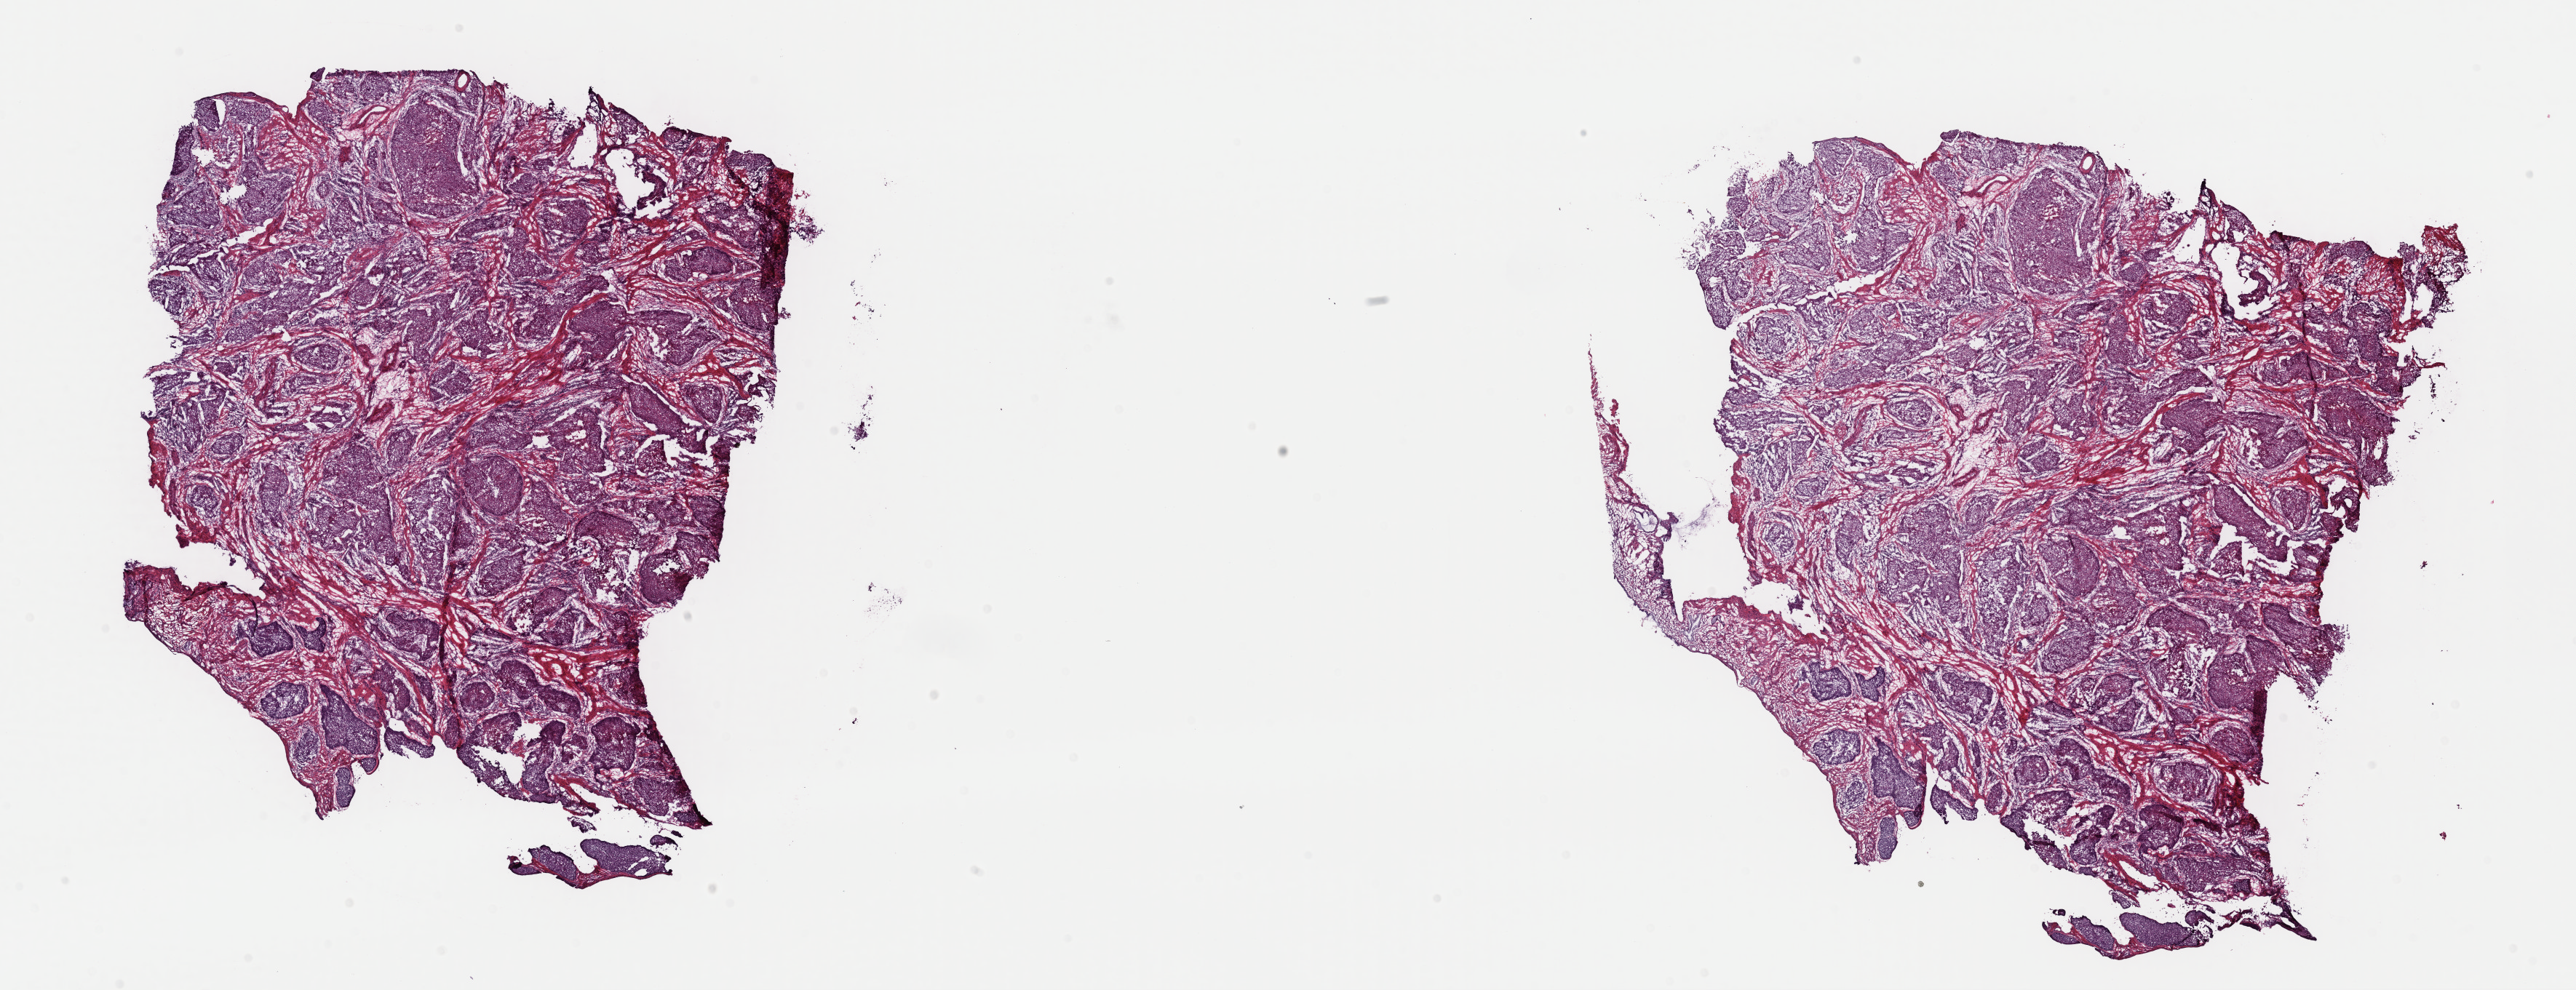
Whole-slide histology image, H&E, whole scanned area (about 28.0 x 10.7 mm) shown as a low-resolution overview, frozen section, sample: primary tumour, cervix. Patient: female, age at initial diagnosis 27 years. Histologic grade: G2 (moderately differentiated). Pathologist review of this section (percent, as recorded): tumour cells 80%, tumour nuclei 80%, normal cells 0%, stromal cells 15%, necrosis 5%. Infiltration values recorded for this section: lymphocyte infiltration 0%, monocyte infiltration 0%, neutrophil infiltration 0%.
• lymph nodes positive (case pathology): 0 of 17 examined
• histologic diagnosis: Squamous cell carcinoma, large cell, nonkeratinizing, NOS (cervix uteri)
• FIGO stage: IIA1